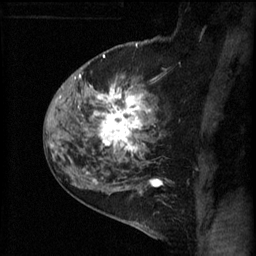
Breast MRI (dynamic contrast-enhanced), one sagittal slice; 3 images stored at this slice position (order not interpretable as contrast timing); 1.5 T; TE 4.2 ms, TR 11 ms; 256 × 256 image matrix, field of view 180 × 180 mm. Female patient, age 52 years.
Structures marked on this image (semi-automatic segmentation, software-assisted and operator-edited):
- analysis volume of interest (the breast-tissue region the enhancement analysis was run in; not a lesion): bounding box (x1, y1, x2, y2) in pixels: (86, 76, 165, 157)
- tumour enhancement mask (voxels above the 70 % enhancement threshold inside the analysis volume of interest): (86, 84, 150, 157)